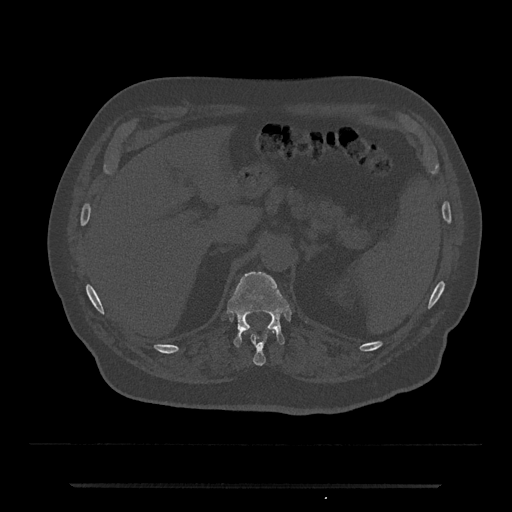
CT including the spine, one axial slice. Slice 613 of 797 in the series (ordered by position). Reconstruction kernel Br40s/3. Bone window (W 1800 / L 400 HU). 0.5 mm slice thickness. 512 × 512 image matrix, field of view 434 × 434 mm. Patient: male, 80 years. From the clinical record (not read from this slice): primary cancer: prostate; vertebrae with lytic lesions (as recorded): L1, T11.
Structures marked on this image (semi-automatic segmentation, software-assisted and operator-edited):
- T11 vertebra: box from (x=251, y=335) to (x=266, y=366) px
- T12 vertebra: (x=228, y=271)–(x=289, y=347)